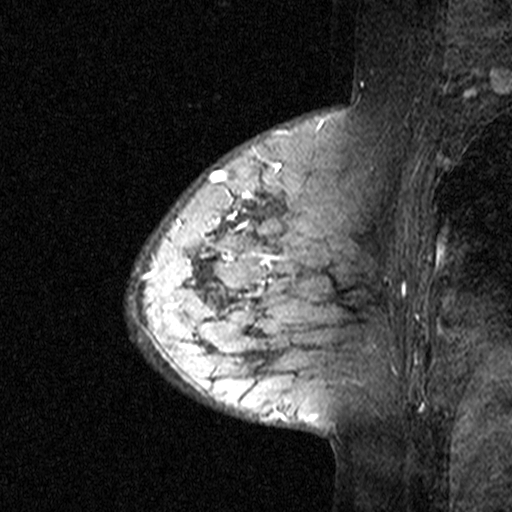
Breast MRI (dynamic contrast-enhanced), one sagittal slice. Position 11 of 44 along the scan axis. Dynamic contrast-enhanced study with each time point stored as its own series, time point 3 of 4 at this slice position (ordered by acquisition time). 1.5 T. TE 4.5 ms, TR 11 ms. 3 mm slice thickness. 512 × 512 image matrix. Female patient, age 65 years. Case-level facts recorded for this patient, not image findings: setting: breast cancer imaged before/during neoadjuvant chemotherapy; receptor status: HER2-positive.
Annotated regions visible in this slice (semi-automatically segmented with operator editing):
- analysis volume of interest (the breast-tissue region the enhancement analysis was run in; not a lesion): bounding box <182,190,353,361> (left, top, right, bottom; pixels)
- tumour enhancement mask (voxels above the 90 % enhancement threshold inside the analysis volume of interest): <190,193,273,313>